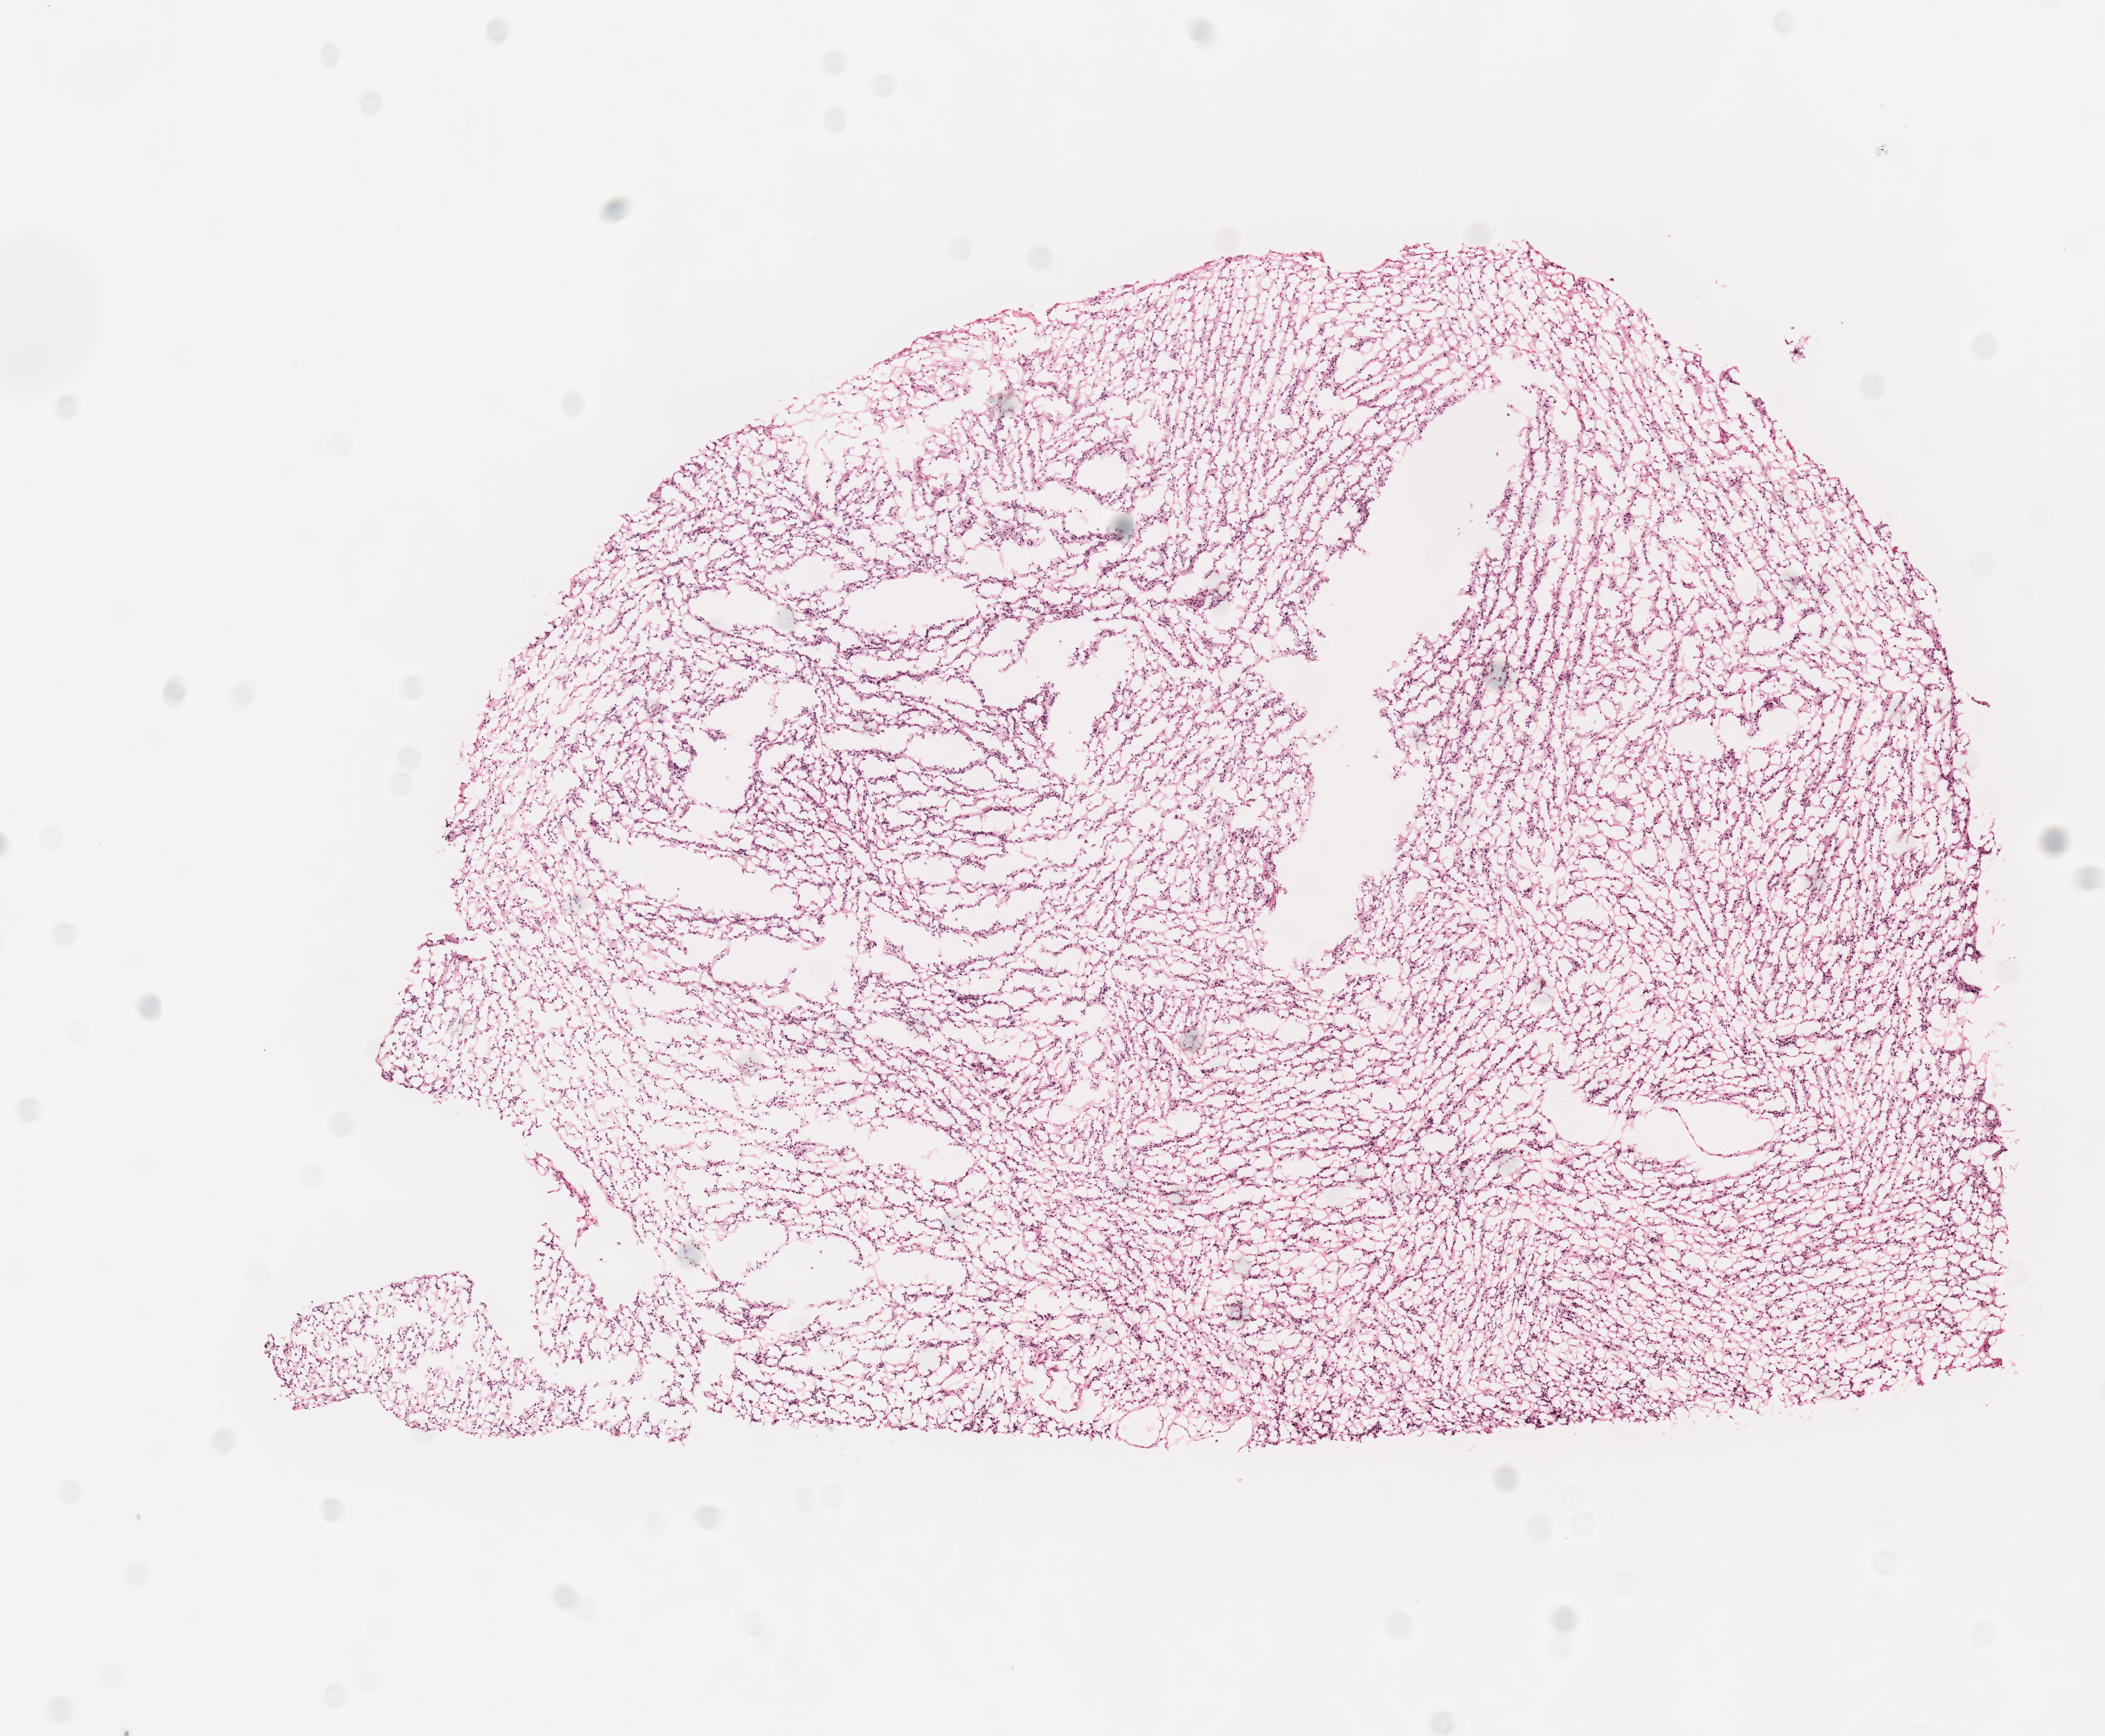
Hematoxylin and eosin (H&E) stained whole-slide image — a low-resolution overview of the entire scanned area, about 6.4 x 5.2 mm, frozen section from the top of the tissue portion, brain, primary tumour sample. Patient: male, age at initial diagnosis 49 years. Histologic grade: G2 (moderately differentiated). Composition of this section per pathologist review: tumour cells 100%, tumour nuclei 75%, normal cells 0%, stromal cells 0%, necrosis 0%.
Histologic diagnosis: Mixed glioma (cerebrum).